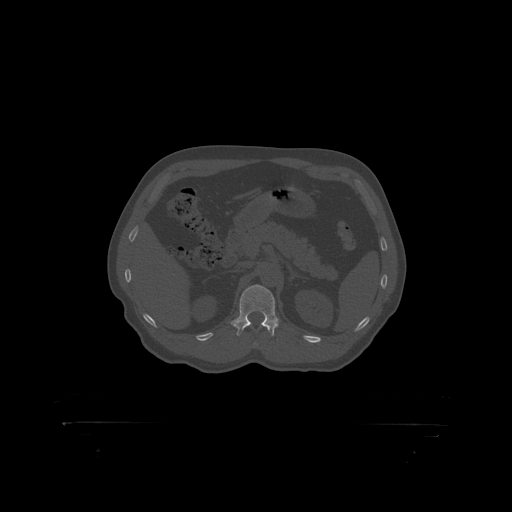
CT including the spine, one axial slice. Position 331 of 399 along the scan axis. 120 kVp. Bone window (W 1800 / L 400 HU). 512 × 512 image matrix. Patient: male, 46 years. Case-level facts recorded for this patient, not image findings: primary cancer: skin.
Structures marked on this image (semi-automatic segmentation, software-assisted and operator-edited):
- L1 vertebra: bounding box [x1, y1, x2, y2] px = [240, 285, 276, 319]